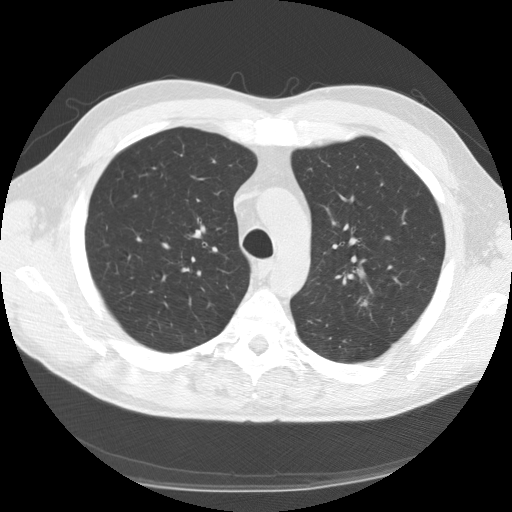
Chest CT (low-dose screening protocol), one axial image; second screening round (one year after baseline); lung window (W 1500 / L -600 HU); 2.5 mm slice thickness; standard (soft-tissue) reconstruction kernel (STANDARD); 120 kVp; slice 38 of 152 in the series. Male participant, aged 57 years at enrolment. Current smoker at enrolment.
- Expert-annotated lung lesion, bounding box <340,286,380,322> (left, top, right, bottom; pixels).
- The exam's reader record, not a measurement of the box and not confirmed to be the same lesion: non-calcified nodule or mass ≥4 mm, left upper lobe, 12 × 7 mm, spiculated (stellate) margins, mixed attenuation, pre-existing on the prior screen: no.
- Official screen result: positive, other.
- Participant outcome: lung cancer diagnosed 419 days after this screen (after the third annual screen) — adenosquamous carcinoma, left upper lobe, poorly differentiated (G3), stage IA (AJCC 6th edition), 15 mm at pathology.